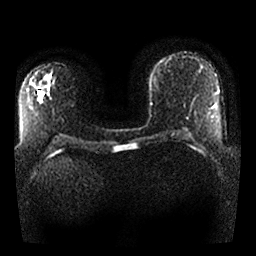
Breast MRI, one axial slice; slice 13 of 25 in the series (ordered by position); diffusion-weighted series; image 2 of 4 stored at this slice position (different b-values; order by instance number); 1.5 T; 256 × 256 image matrix, field of view 330 × 330 mm. Female patient.
Outlined on this slice (expert manual segmentation):
- tumour on diffusion-weighted imaging: bounding box [x1, y1, x2, y2] px = [46, 76, 51, 82]